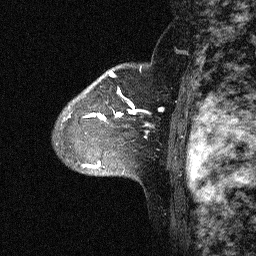
Breast MRI (dynamic contrast-enhanced), one sagittal slice. Slice 47 of 64 in the series (ordered by position). Dynamic contrast-enhanced study with each time point stored as its own series, time point 2 of 3 at this slice position (early post-contrast, ordered by acquisition time). 1.5 T. TE 4.5 ms, TR 11 ms. 2.06 mm slice thickness. 256 × 256 image matrix, field of view 200 × 200 mm. Patient: female, 46 years. Case-level facts recorded for this patient, not image findings: setting: breast cancer imaged before/during neoadjuvant chemotherapy; receptor status: HER2-positive.
Structures marked on this image (semi-automatically segmented with operator editing):
- analysis volume of interest (the breast-tissue region the enhancement analysis was run in; not a lesion): bounding box (x1, y1, x2, y2) in pixels: (43, 72, 164, 177)
- tumour enhancement mask (voxels above the 90 % enhancement threshold inside the analysis volume of interest): (82, 72, 164, 167)